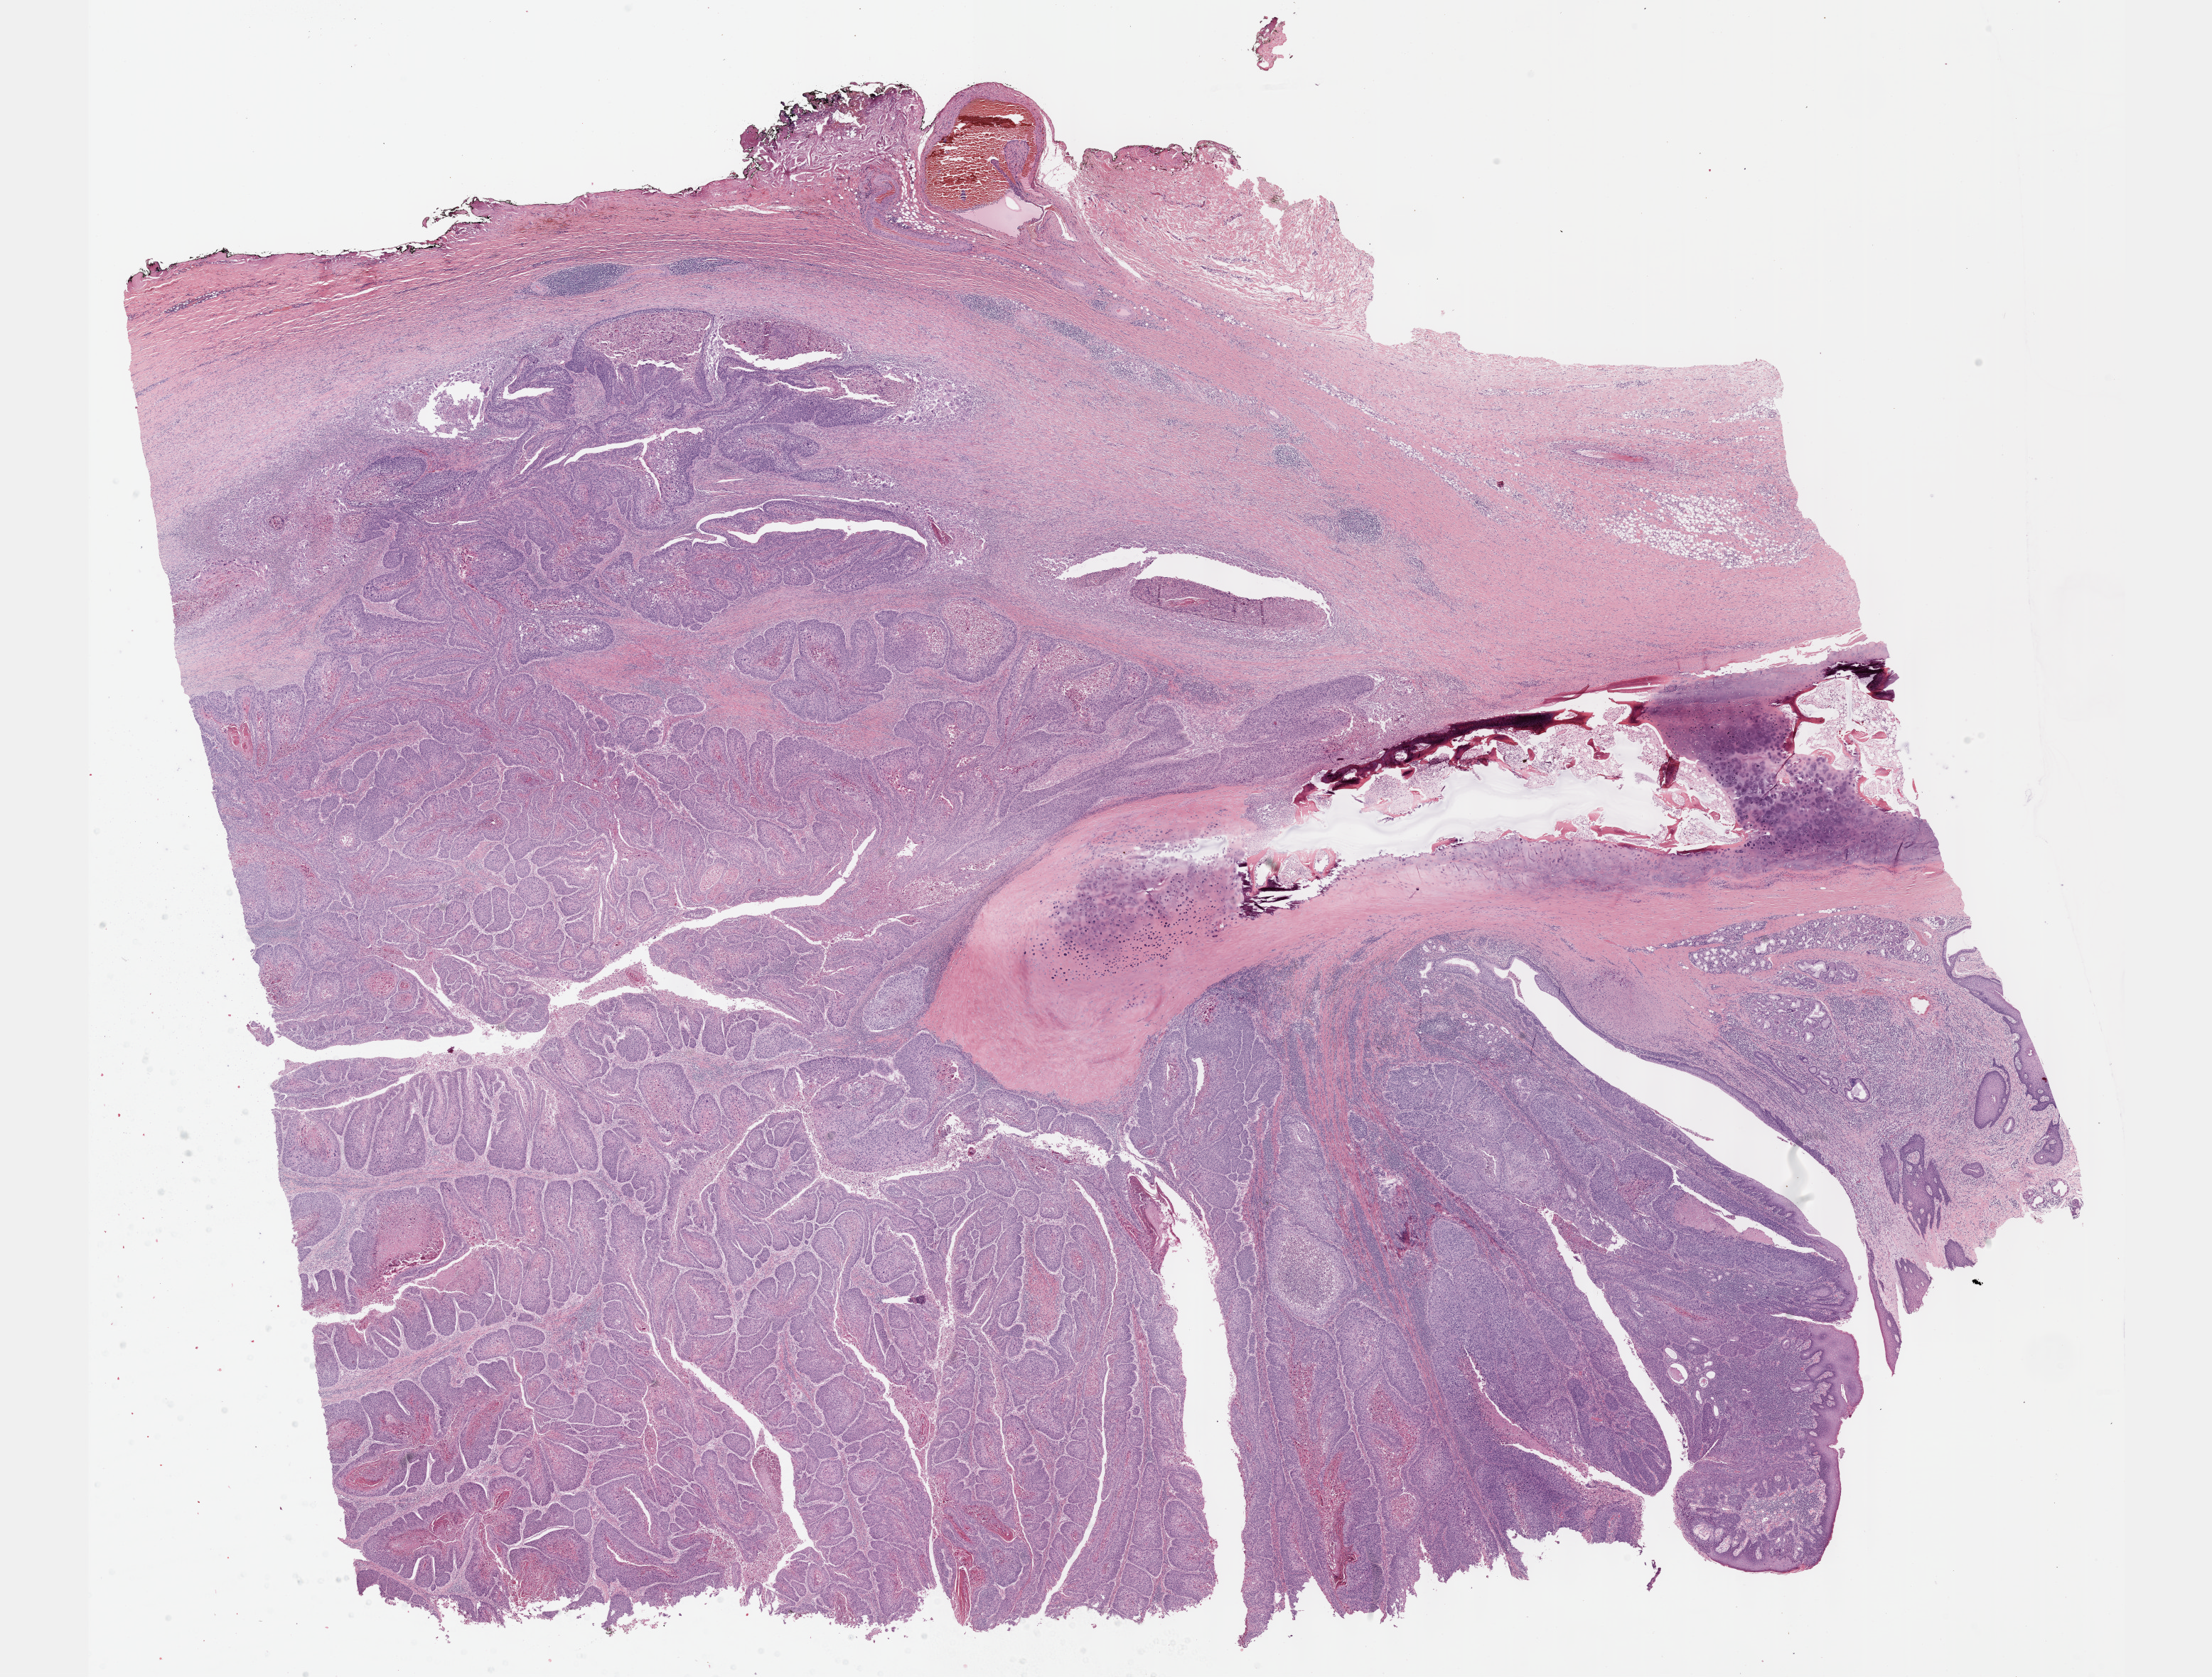
Digitized H&E-stained tissue section (whole slide) — shown as a low-resolution overview of the whole scanned area (about 25.1 x 19.1 mm, acquisition: 40x scan); formalin-fixed paraffin-embedded (FFPE) diagnostic section; head and neck, primary tumour sample. Patient: female, age at initial diagnosis 54 years. Histologic grade: G2 (moderately differentiated).
Laterality: left. AJCC pathologic stage: IVA. Pathologic diagnosis: Squamous cell carcinoma, NOS (larynx, NOS). TNM: T4a N0 M0.